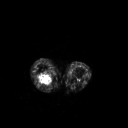
FDG PET of an extremity soft-tissue mass (from a PET/CT study), one axial slice; position 184 of 267 along the scan axis; 3.27 mm slice thickness; 128 × 128 image matrix, field of view 500 × 500 mm. Female patient, age 62 years. Case-level facts recorded for this patient, not image findings: histological type: liposarcoma; site of the primary tumour: right thigh.
Outlined on this slice (expert contour drawn on MRI and transferred to this co-registered scan by the dataset authors):
- gross tumour volume (mass): bounding box [x1, y1, x2, y2] px = [37, 73, 53, 86]